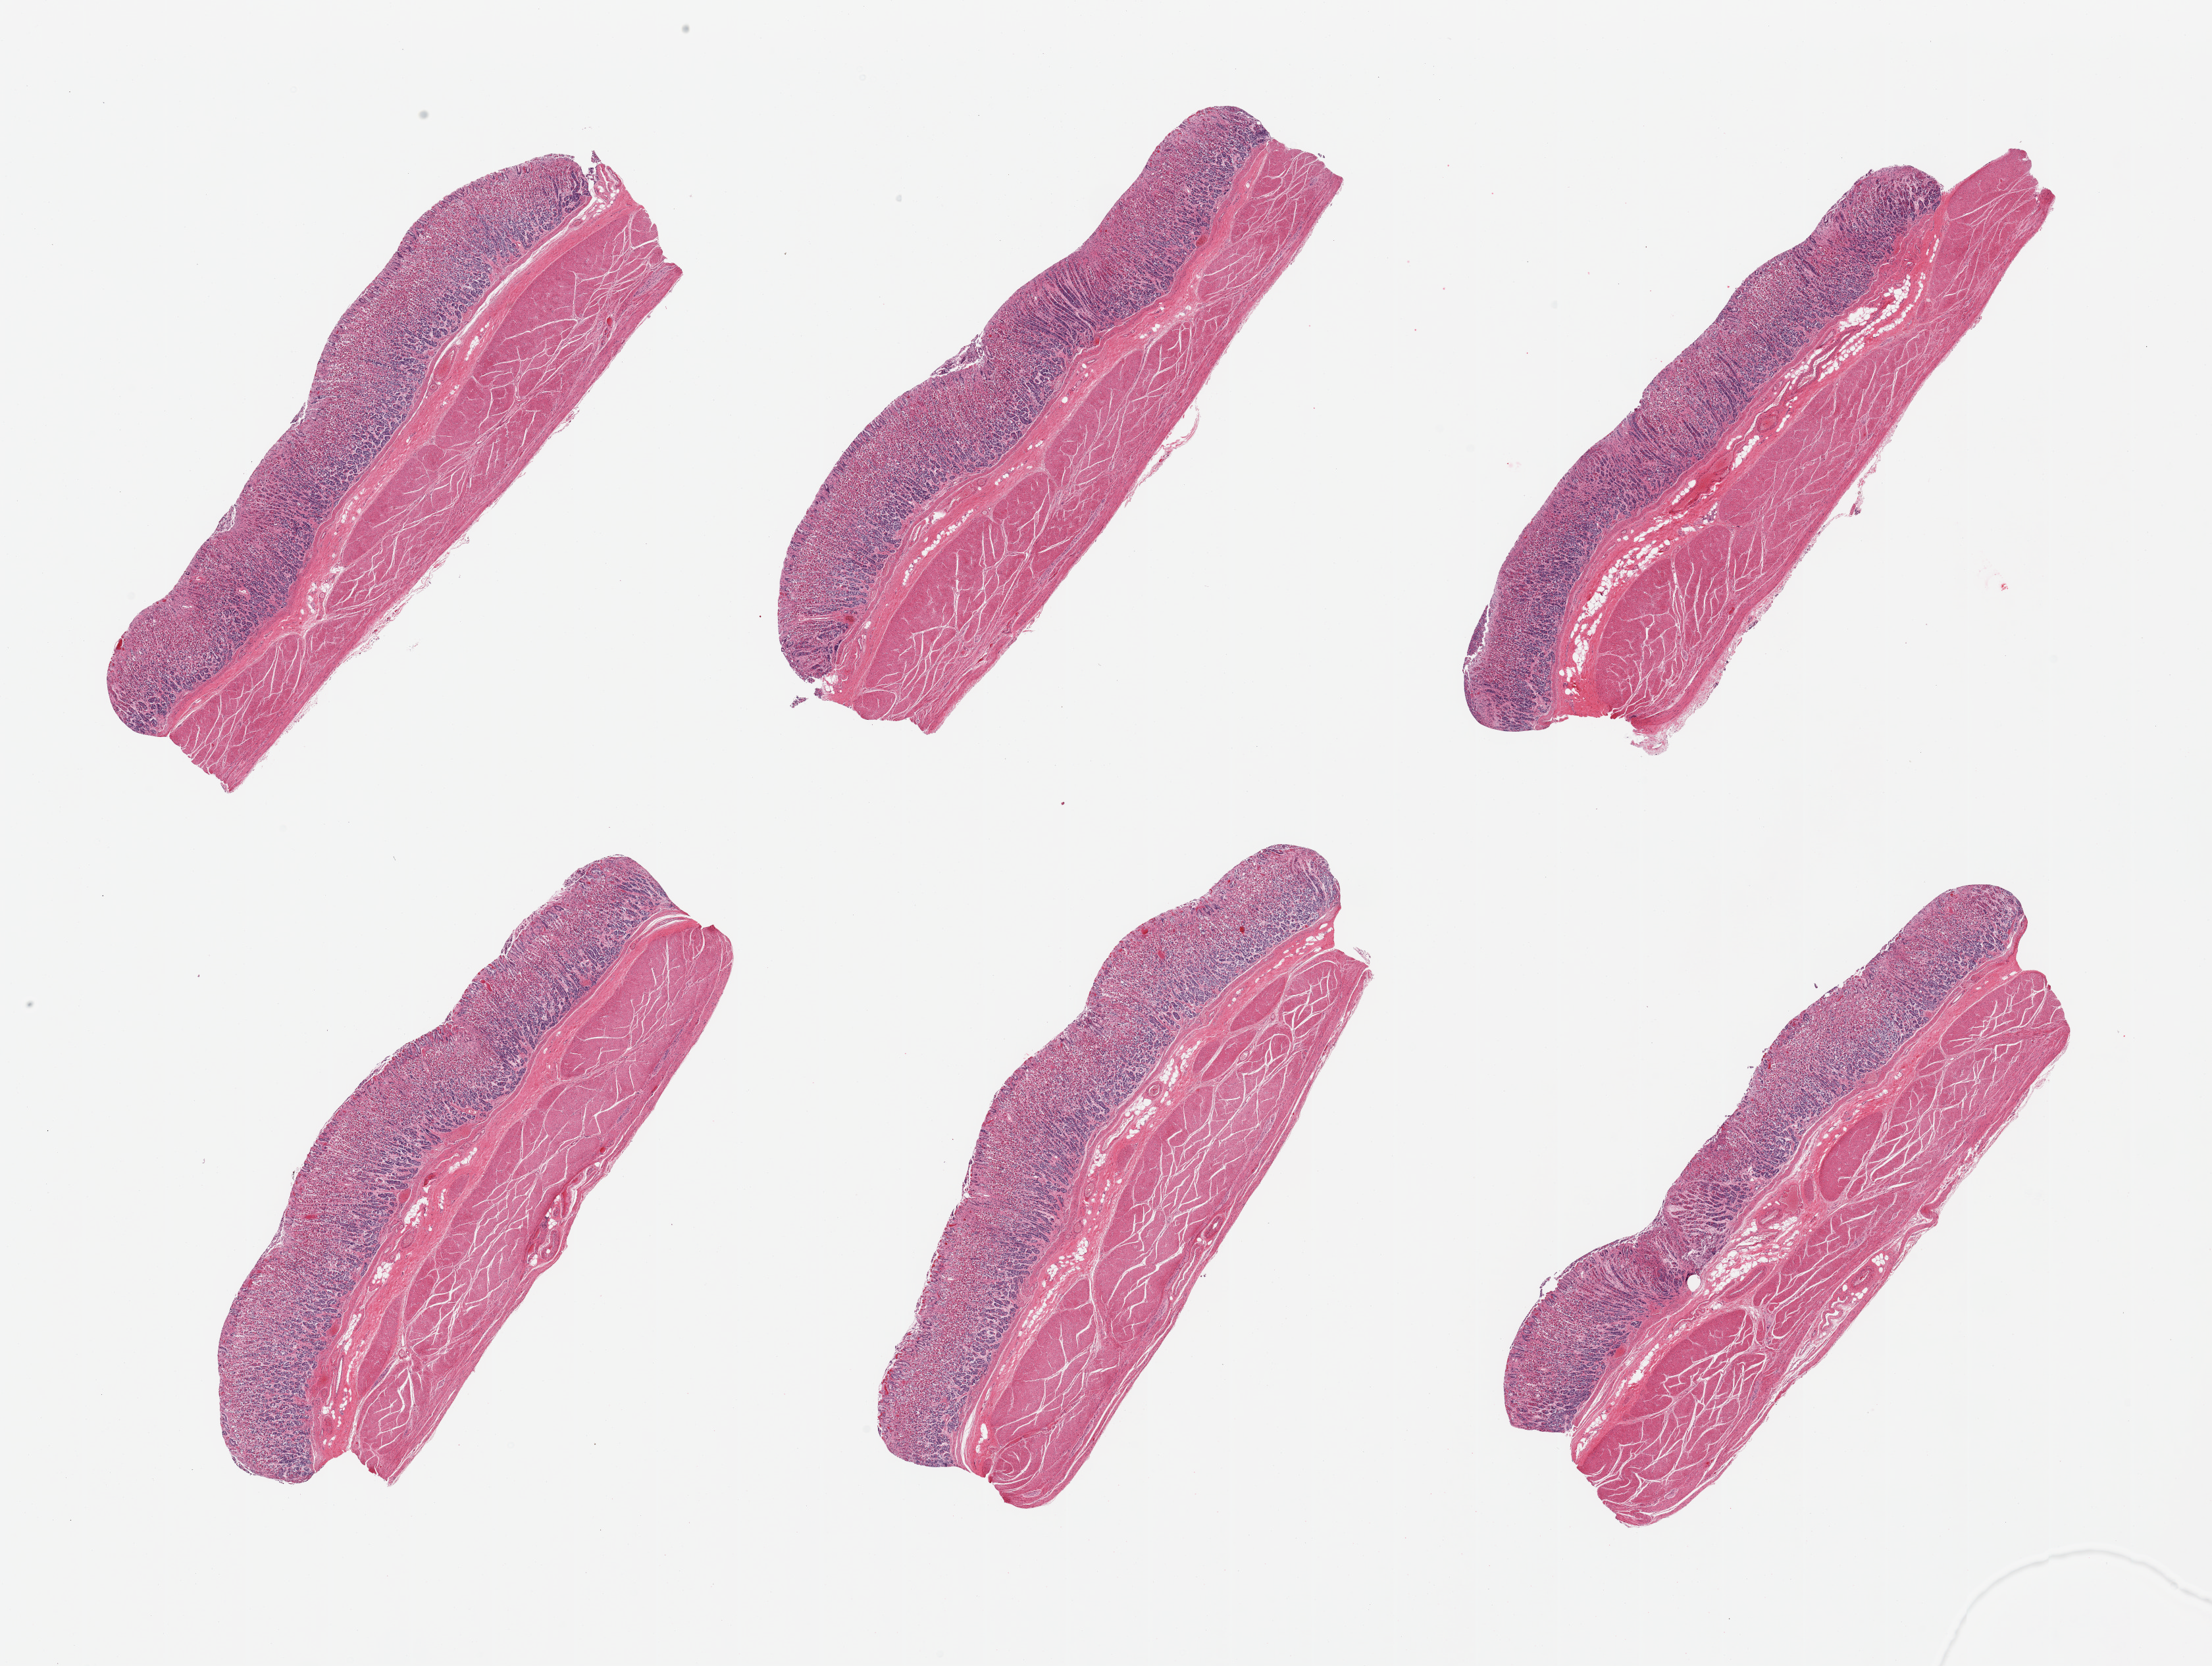
Hematoxylin and eosin (H&E) whole-slide image — shown as a low-resolution overview of the whole scanned area (about 26.6 x 20.0 mm, from a 20x scan), PAXgene-fixed, paraffin-embedded tissue, section of stomach (target tissue), donor tissue sample. Donor sex: male.
Reviewer comment on this tissue sample: 6 pieces.